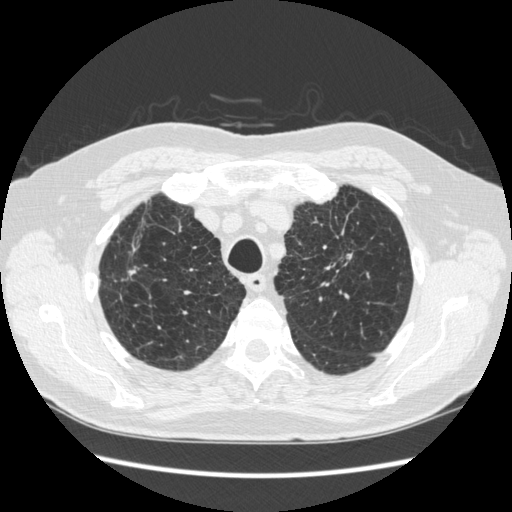
Axial slice from a low-dose chest CT screening exam; third annual screen; lung window (W 1500 / L -600 HU); standard (soft-tissue) reconstruction kernel (STANDARD); slice 51 of 267 in the series. Male participant, aged 70 years at enrolment. Former smoker at enrolment.
Lesion marked by an expert reader, bounding box (x1, y1, x2, y2) in pixels: (322, 212, 371, 276). The screening reader recorded 2 non-calcified nodules or masses ≥4 mm on this exam (left upper lobe, right lower lobe); which of them this box marks is not recorded. Official screen result: positive, other. Participant outcome: lung cancer diagnosed 92 days after this screen — squamous cell carcinoma, NOS, left upper lobe, moderately differentiated (G2), stage IA (AJCC 6th edition), 18 mm at pathology.